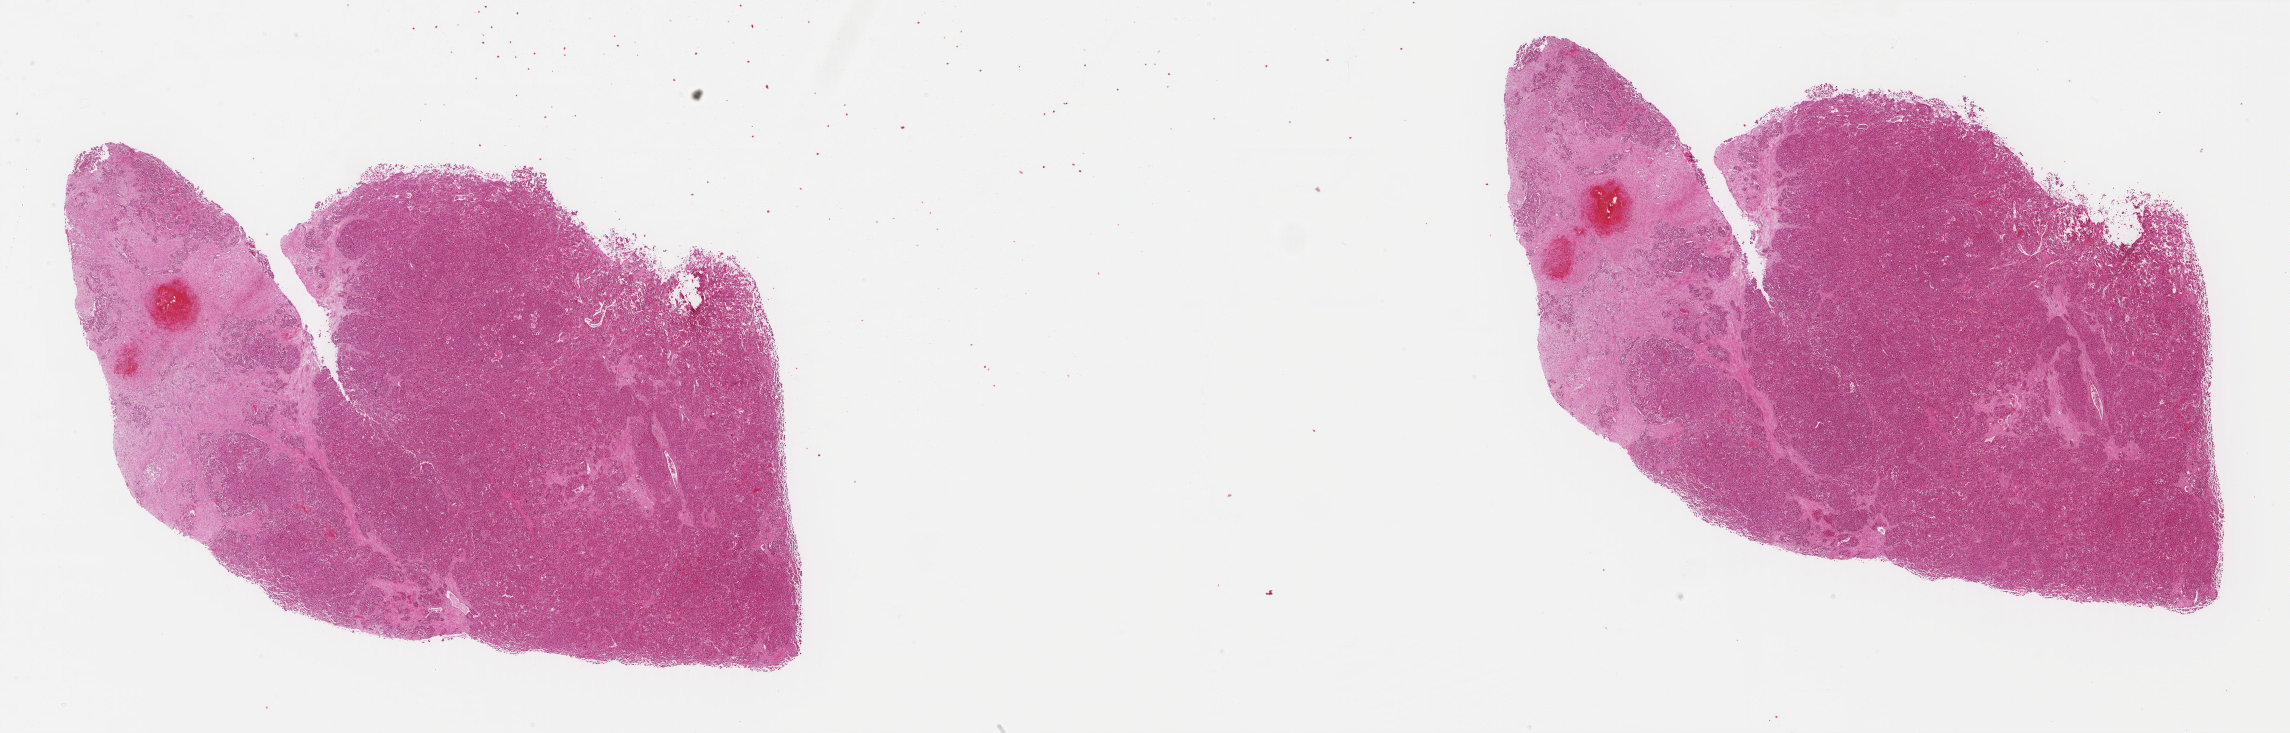
Hematoxylin and eosin (H&E) stained whole-slide image, a low-resolution overview of the entire scanned area, about 36.4 x 11.6 mm (acquisition: 40x scan); formalin-fixed paraffin-embedded (FFPE) diagnostic section; sample: primary tumour, liver. Patient: female, age at initial diagnosis 52 years. Histologic grade: G2 (moderately differentiated).
AJCC pathologic stage: IIIA. TNM: T3a N0 MX. Histologic diagnosis: Hepatocellular carcinoma, NOS.